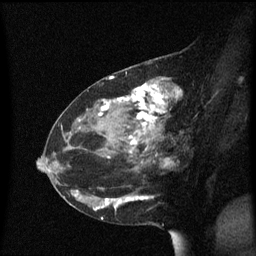
Breast MRI (dynamic contrast-enhanced), one sagittal slice. Slice 30 of 60 in the series (ordered by position). Dynamic contrast-enhanced series, image 2 of 3 at this slice position (ordered by acquisition). 1.5 T. TE 4.2 ms, TR 8.4 ms. 2 mm slice thickness. 256 × 256 image matrix, field of view 200 × 200 mm. Female patient, age 48 years. Case-level facts recorded for this patient, not image findings: setting: breast cancer imaged before/during neoadjuvant chemotherapy; receptor status: HR-positive, HER2-negative.
Annotated regions visible in this slice (semi-automatically segmented with operator editing):
- analysis volume of interest (the breast-tissue region the enhancement analysis was run in; not a lesion): bounding box (x1, y1, x2, y2) in pixels: (80, 78, 183, 221)
- tumour enhancement mask (voxels above the 70 % enhancement threshold inside the analysis volume of interest): (98, 84, 183, 221)